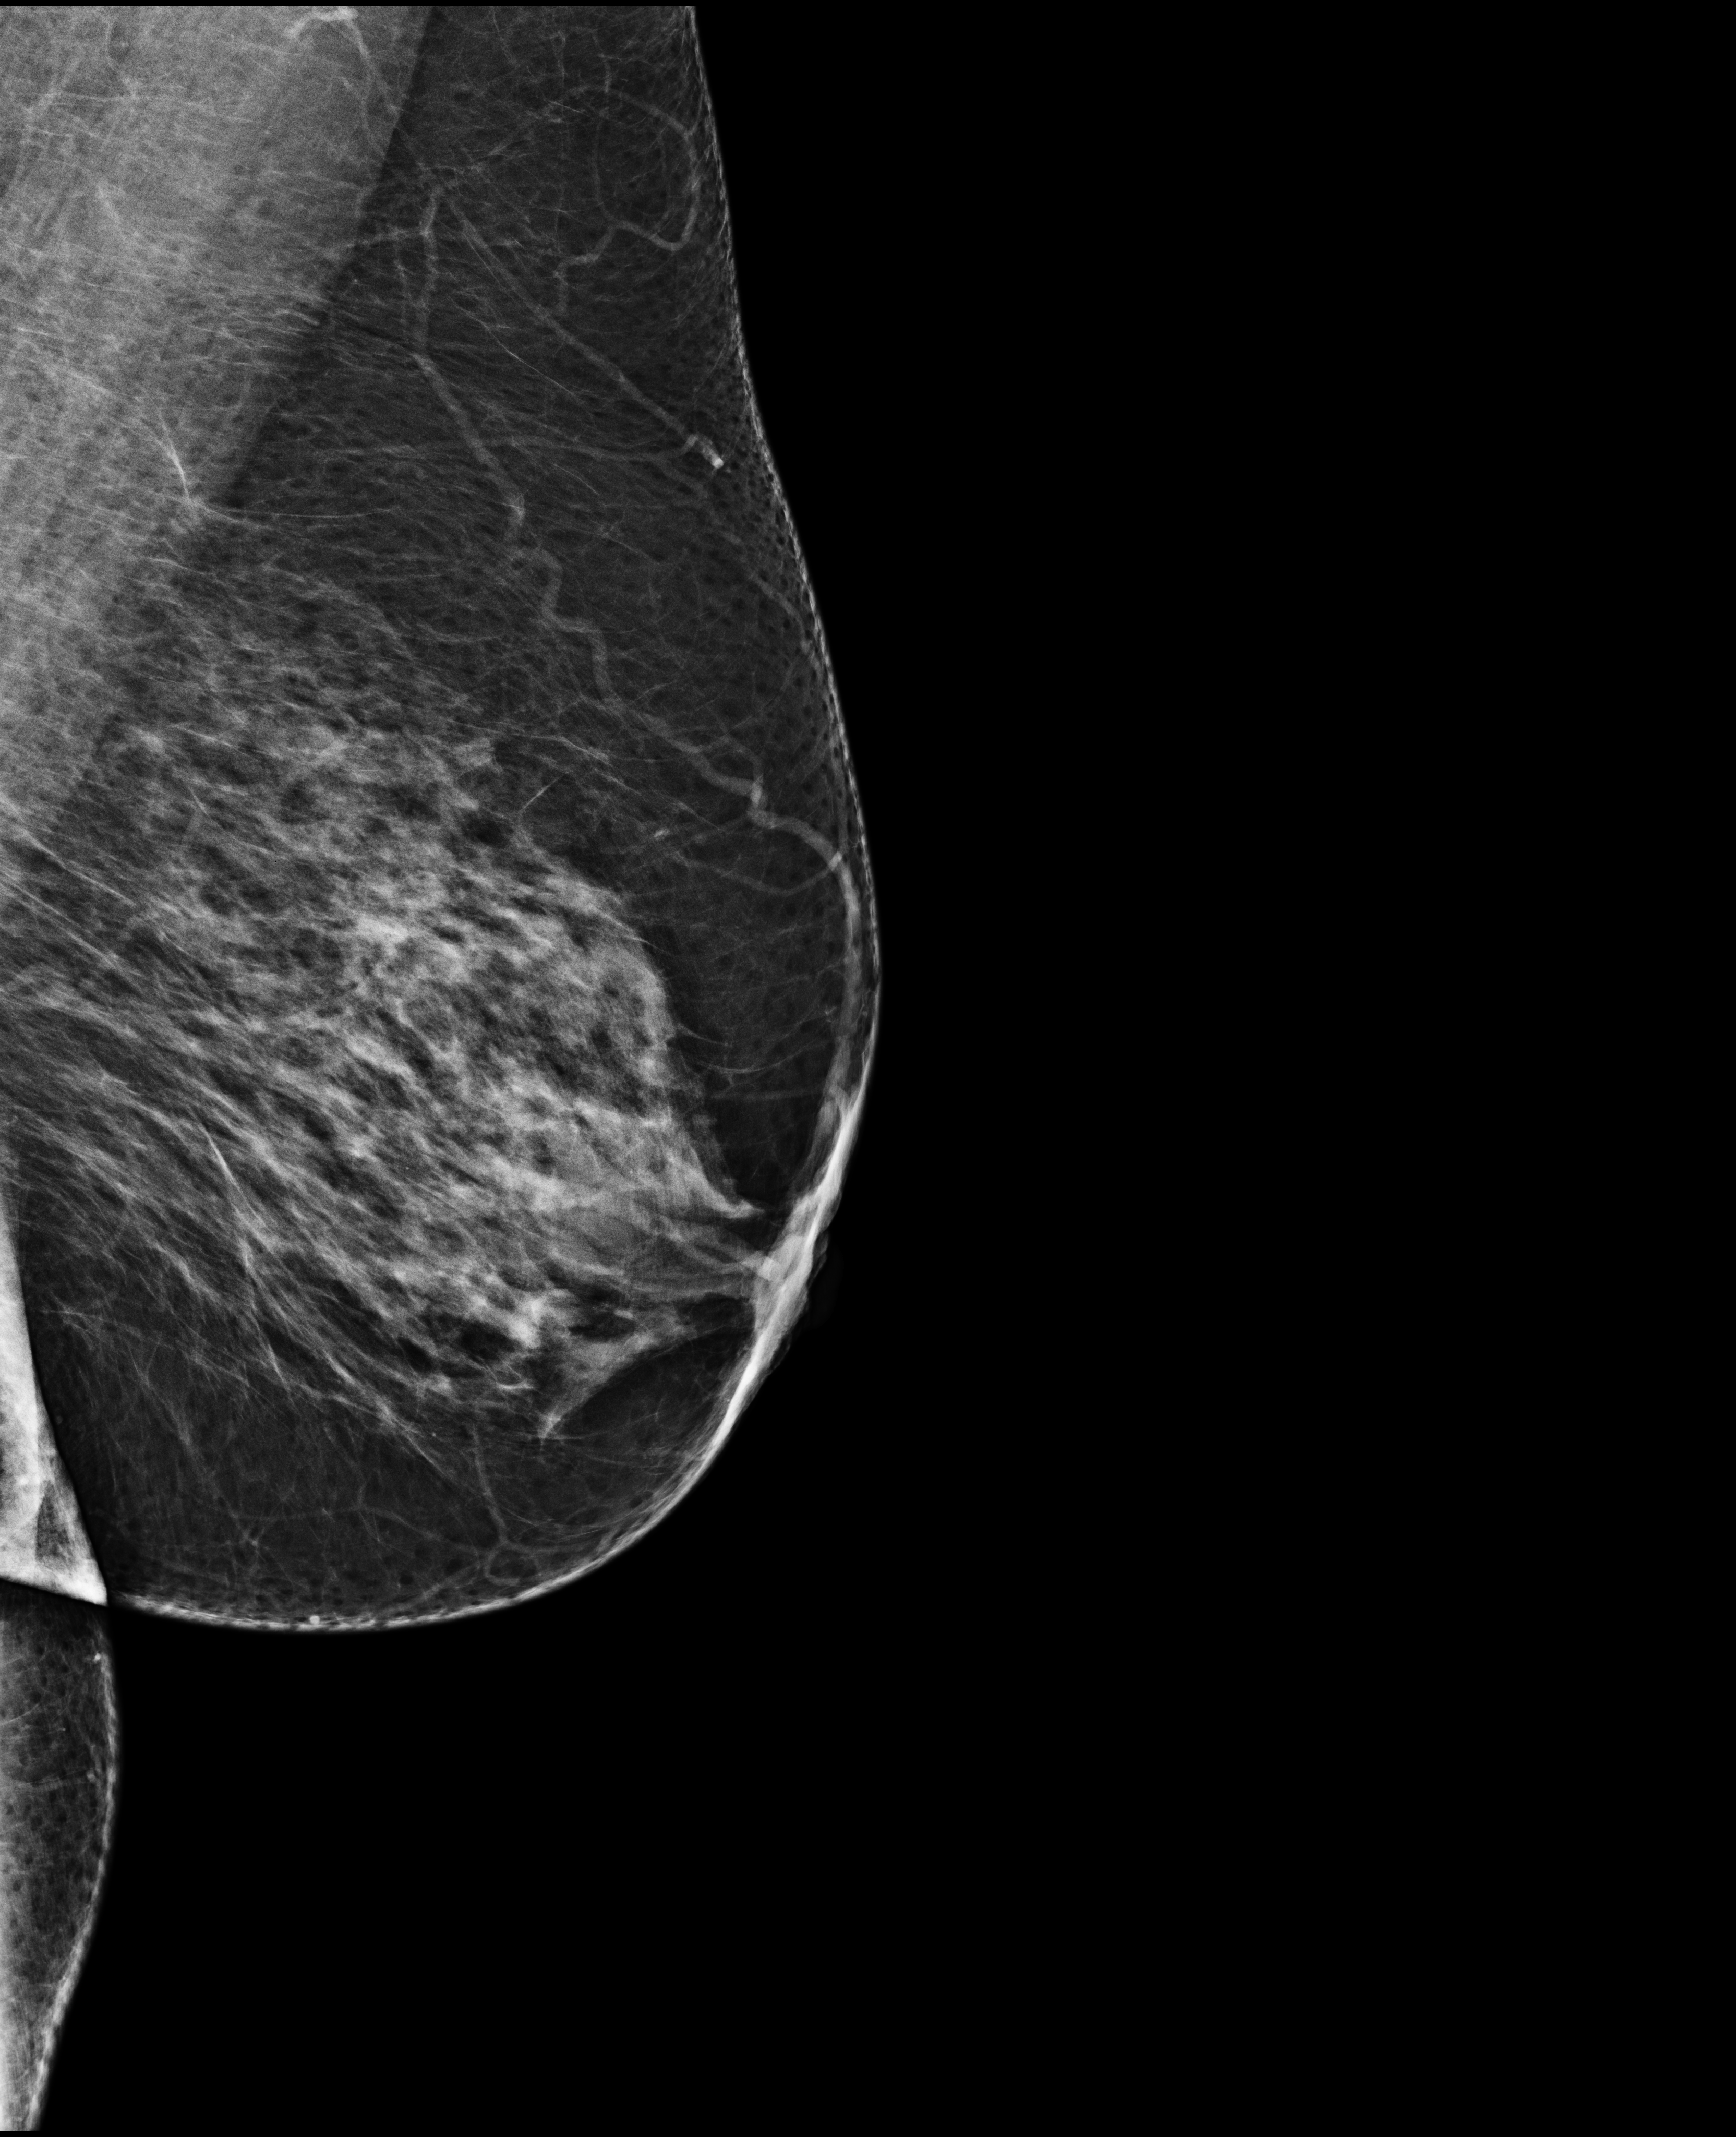
Annual screening mammography examination; compressed breast thickness 74 mm. Patient aged 71 years (female).
Image type: full-field digital mammogram. Breast: left. Projection: medio-lateral oblique projection. BI-RADS breast density category at the screening exam (both breasts, scale 1–4): 3. Final BI-RADS category for the screening round (tomosynthesis exam, both breasts): category 2. Recall: no recall after this screen.